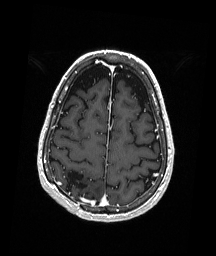
Brain MRI from a brain-tumour surgery series, one axial slice; slice 59 of 192 in the series (ordered by position); T1-weighted post-contrast; 1 mm slice thickness; 216 × 256 image matrix, field of view 211 × 250 mm. From the clinical record (not read from this slice): histopathology: Astrocytoma; WHO grade: 3; IDH mutation: yes.
Outlined on this slice (outlined manually by an expert reader):
- previous resection cavity: box from (x=65, y=171) to (x=88, y=196) px